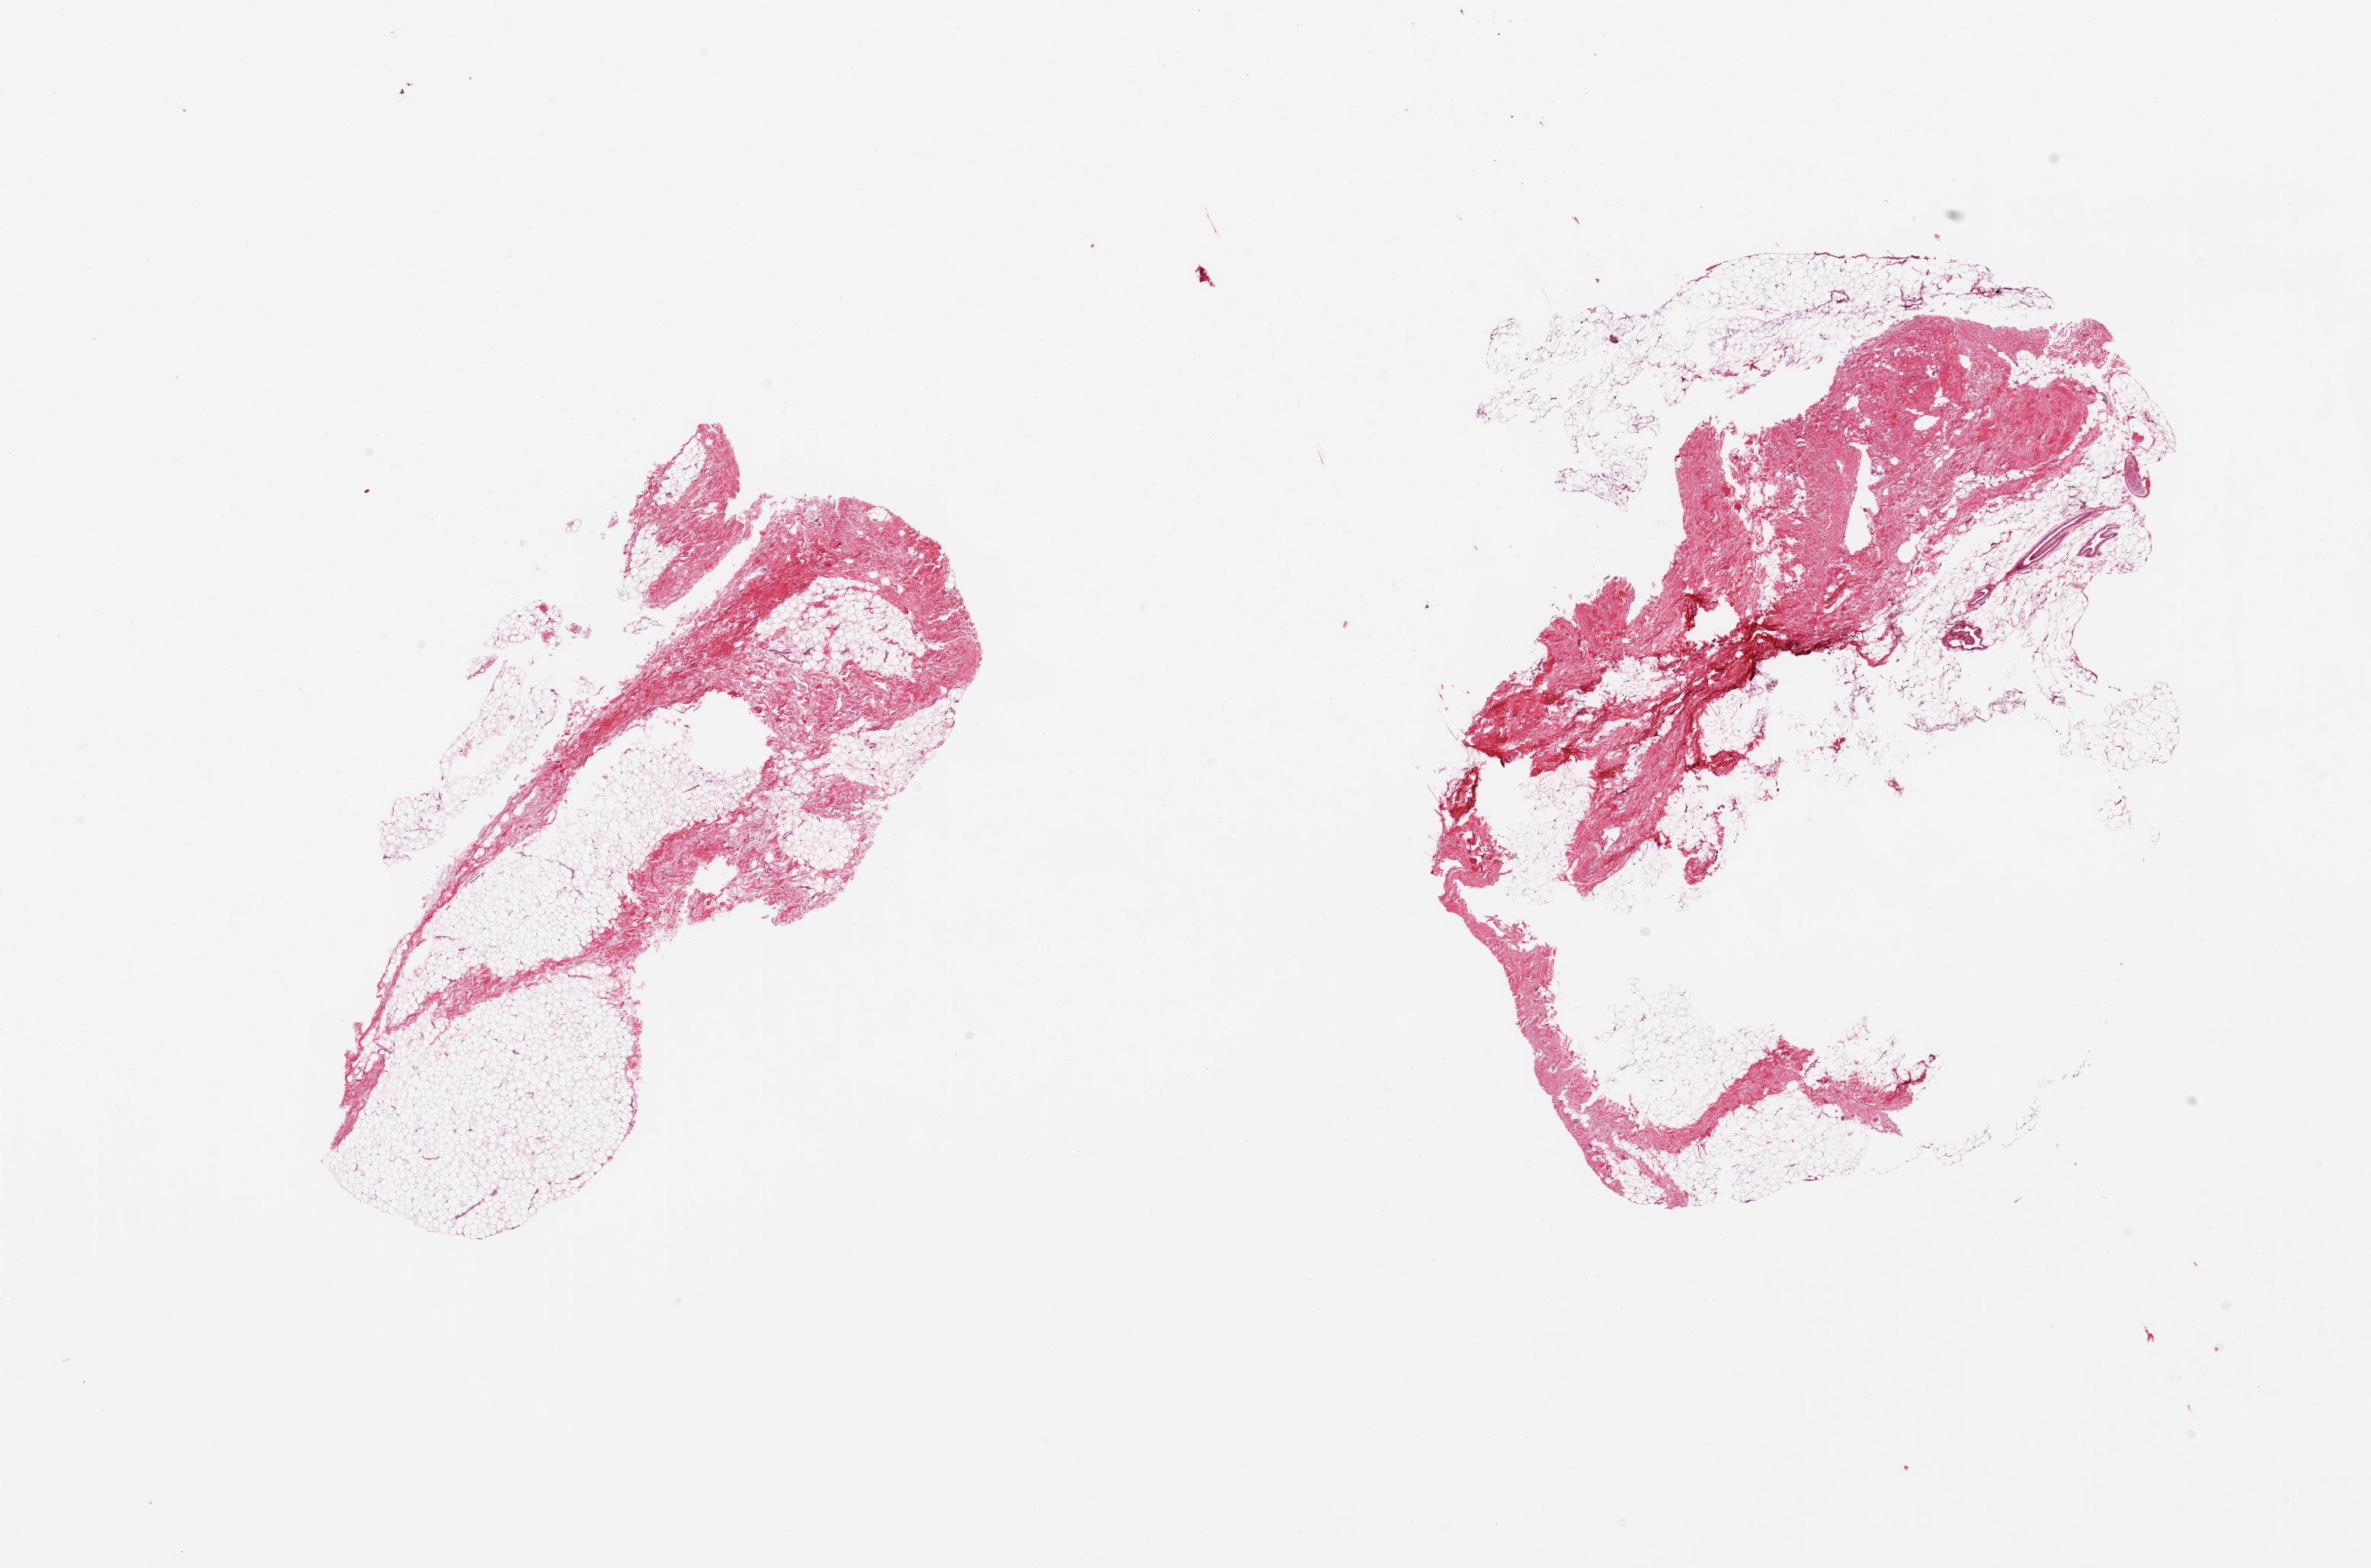
Hematoxylin and eosin (H&E) whole-slide image, brightfield — whole scanned area (about 24.6 x 16.3 mm) shown as a low-resolution overview; PAXgene-fixed paraffin-embedded (PFPE) section; section of breast (target tissue); tissue donor sample. Donor: male.
Review note (as recorded): 2 pieces; fibrofatty tissue without mammary ducts.